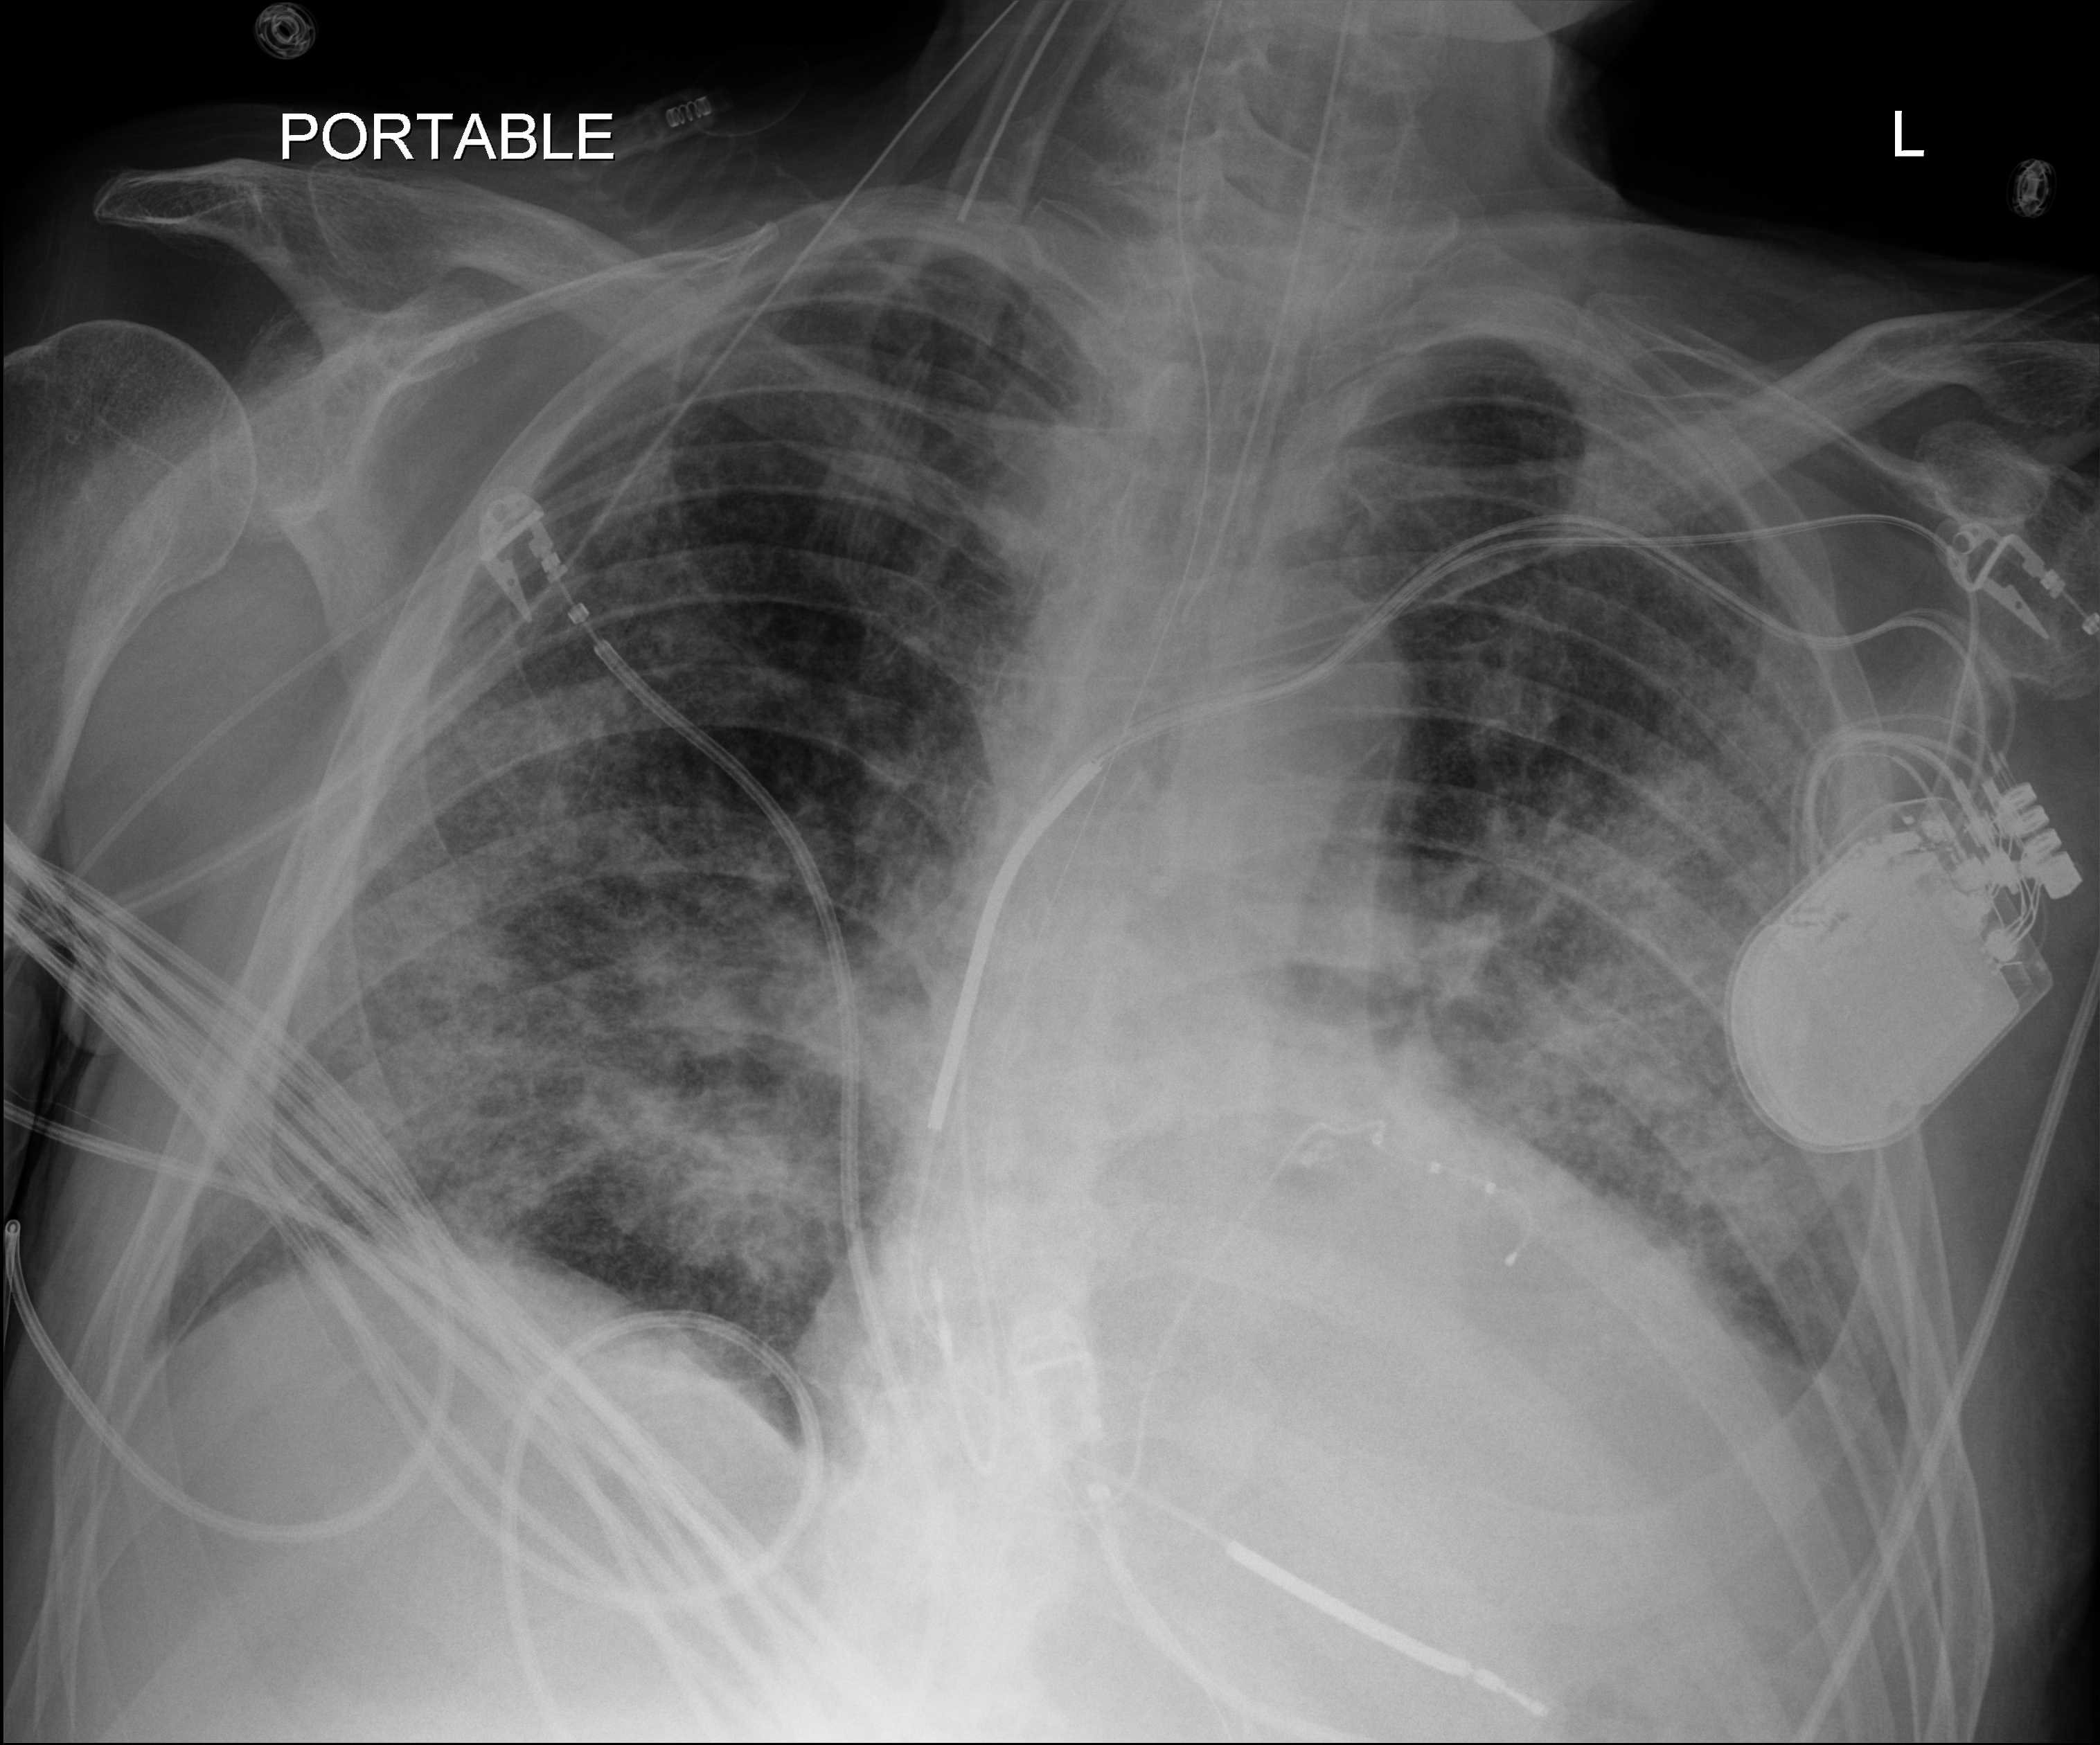
Bedside chest radiograph (digital radiography), anteroposterior (AP) projection. Patient hospitalised with COVID-19; male, aged 60–74 years.
Admission-level facts for this patient (not findings on this image; timing relative to this image not recorded): admitted to intensive care during this hospital stay: yes.